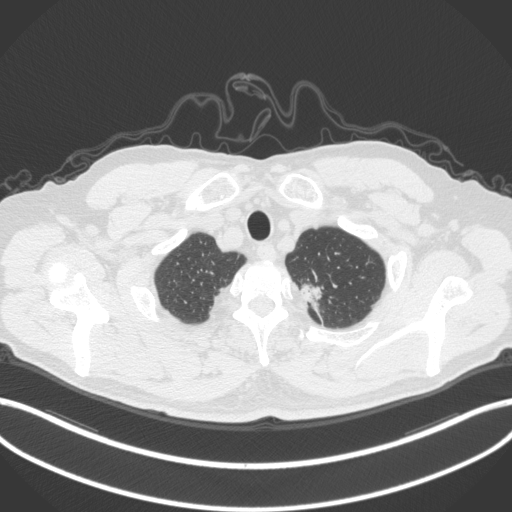
Chest CT, one axial slice; slice 347 of 382 in the series (ordered by position); reconstruction kernel B31f; lung window (W 1500 / L -600 HU); 1 mm slice thickness; 512 × 512 image matrix, field of view 400 × 400 mm. Male patient, age 64 years. From the clinical record (not read from this slice): clinical TNM (as recorded): T1c N0 M0.
Structures marked on this image (bounding box drawn by a radiologist):
- lung tumour (recorded histology: adenocarcinoma): bounding box [x1, y1, x2, y2] px = [298, 278, 326, 307]